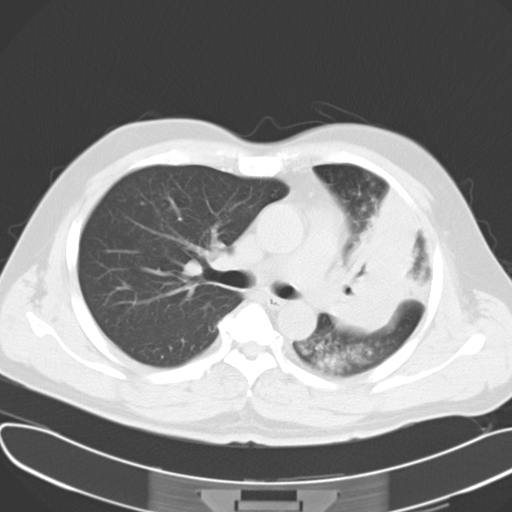
Chest CT, one axial slice. Position 20 of 30 along the scan axis. Lung window (W 1500 / L -600 HU). 10 mm slice thickness. 512 × 512 image matrix, field of view 377 × 377 mm. Patient: male, 48 years. Case-level facts recorded for this patient, not image findings: clinical TNM (as recorded): T4 N0 M0.
Structures marked on this image (rectangle marked by the reading radiologist):
- lung tumour (recorded histology: adenocarcinoma): bounding box [x1, y1, x2, y2] px = [334, 189, 419, 343]